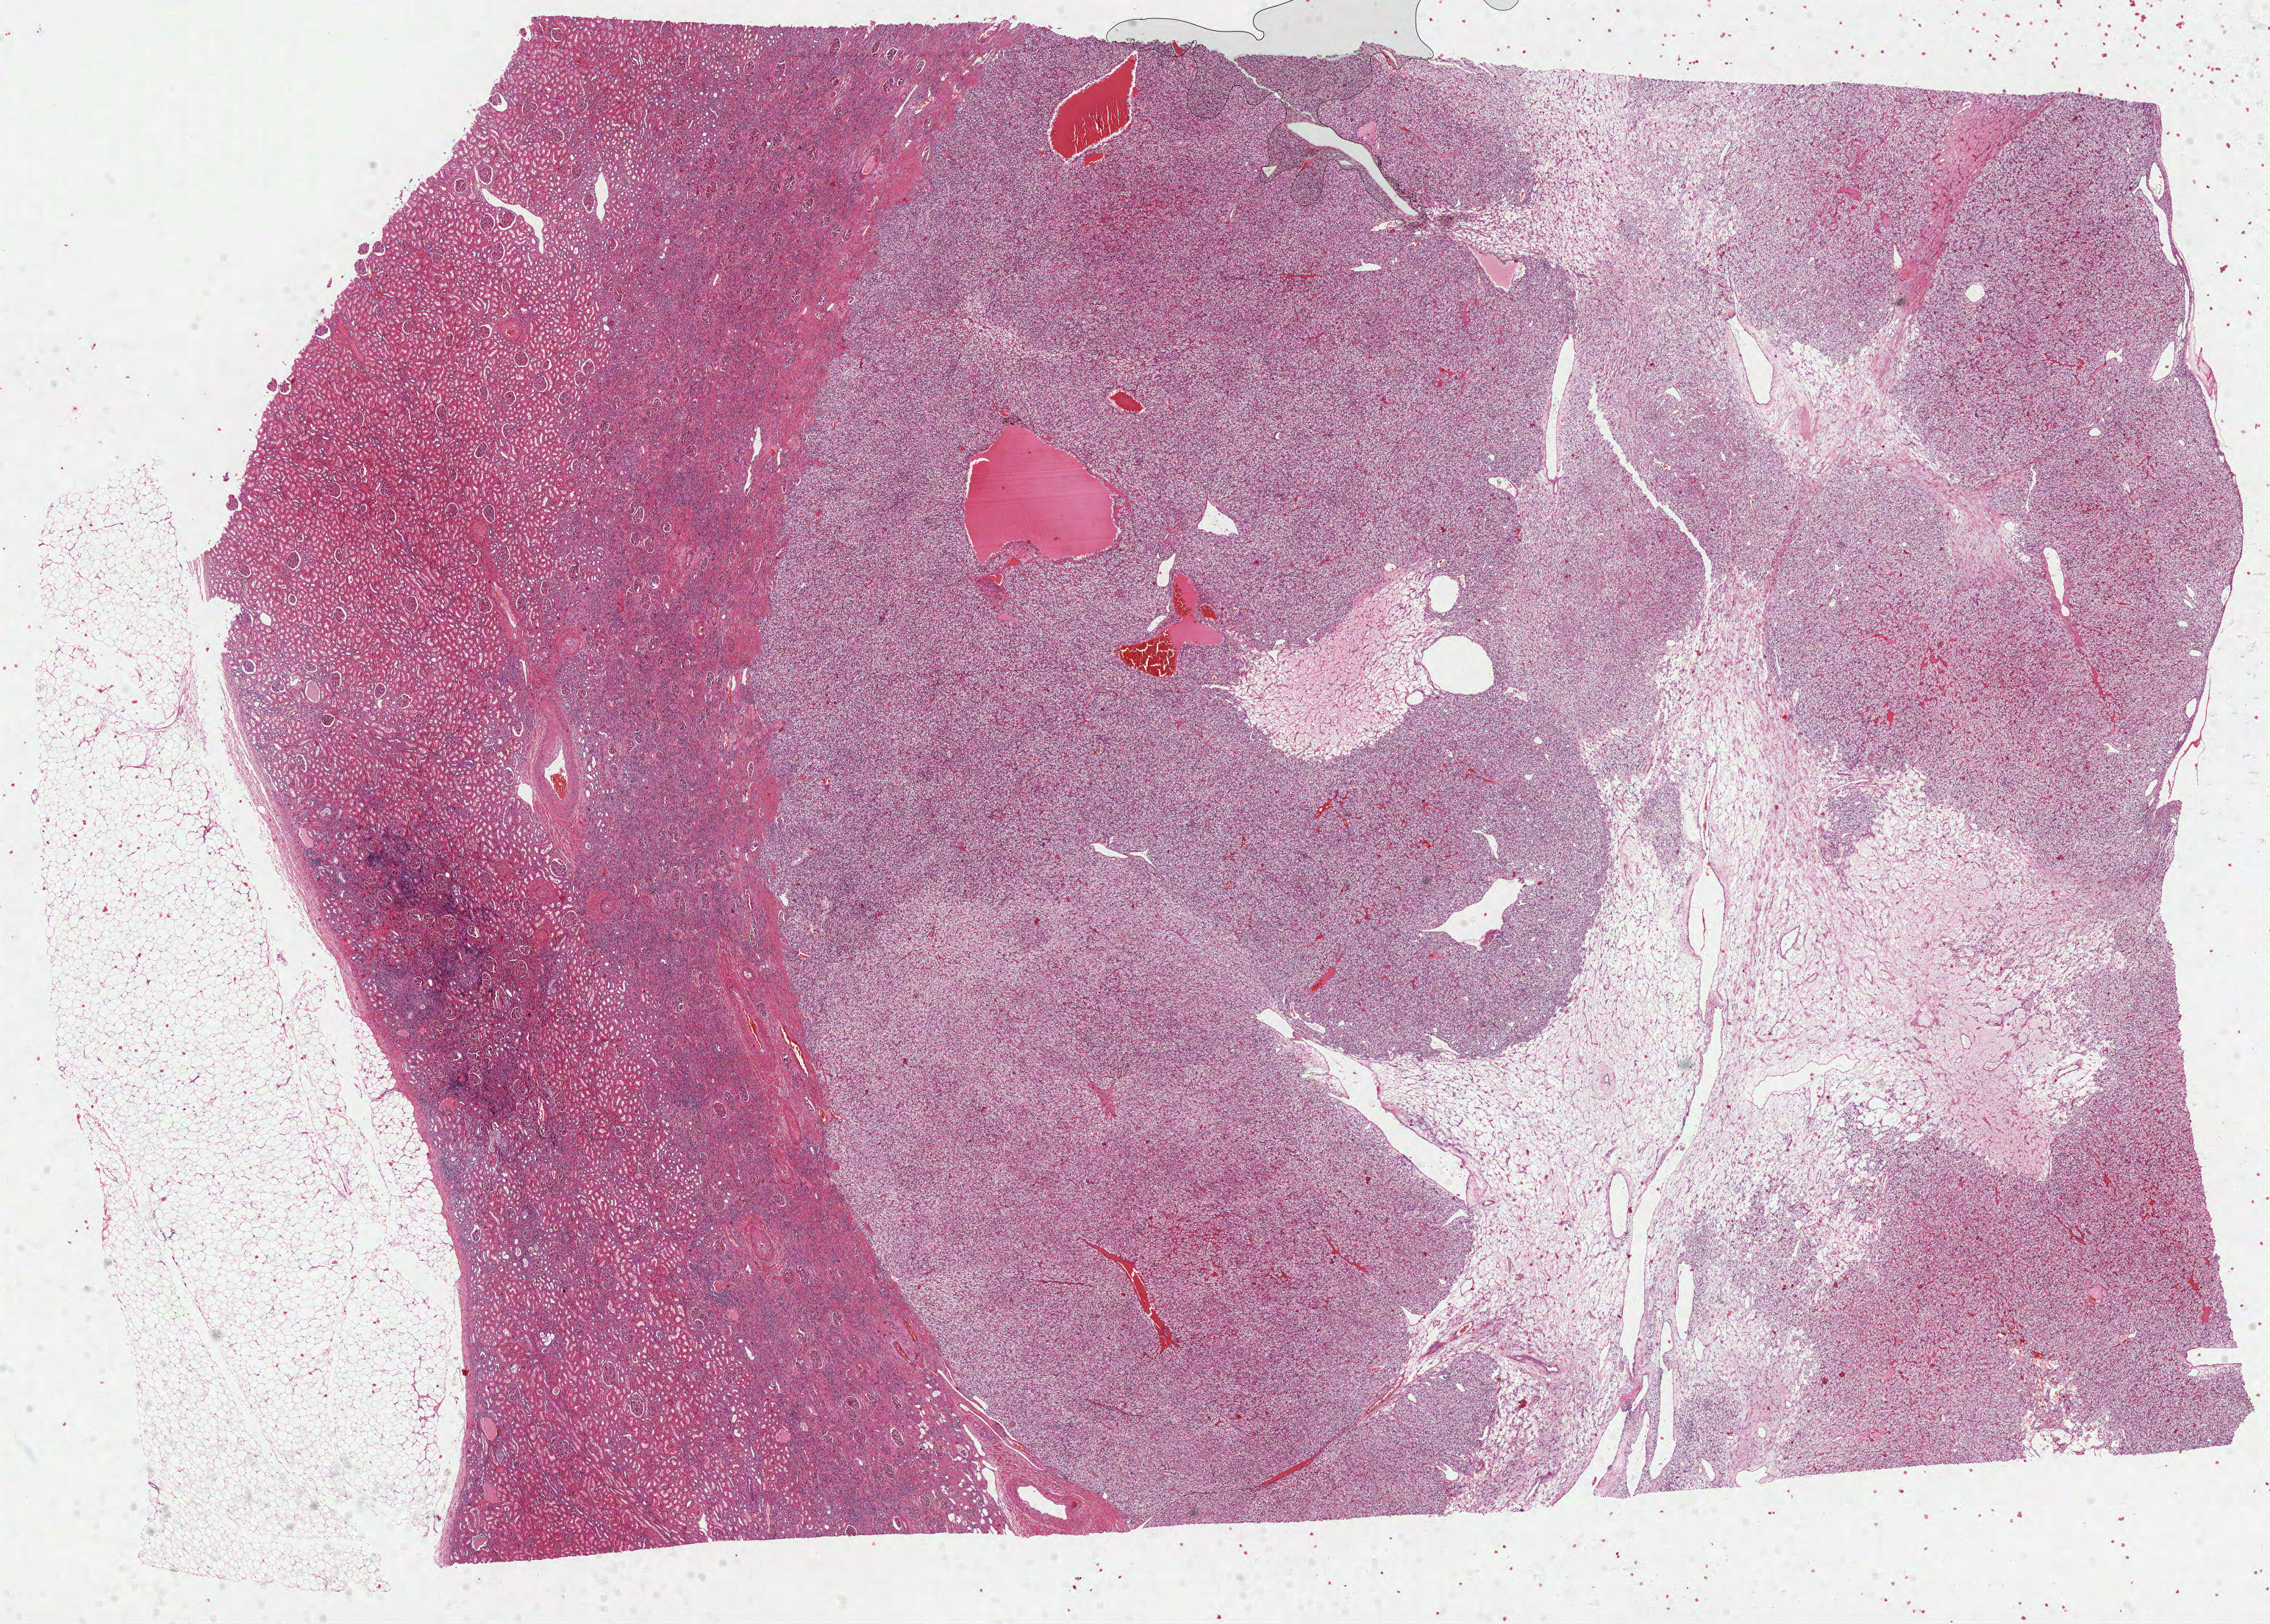
Digitized H&E tissue section (whole slide), a low-resolution overview of the entire scanned area, about 24.9 x 17.8 mm (slide scanned at 40x). Formalin-fixed paraffin-embedded (FFPE) diagnostic section. Kidney, primary tumour sample. Male patient; age at initial diagnosis 53 years. Histologic grade: G2 (moderately differentiated).
Diagnosis: Clear cell adenocarcinoma, NOS. Laterality: left. AJCC pathologic stage: I (6th edition).